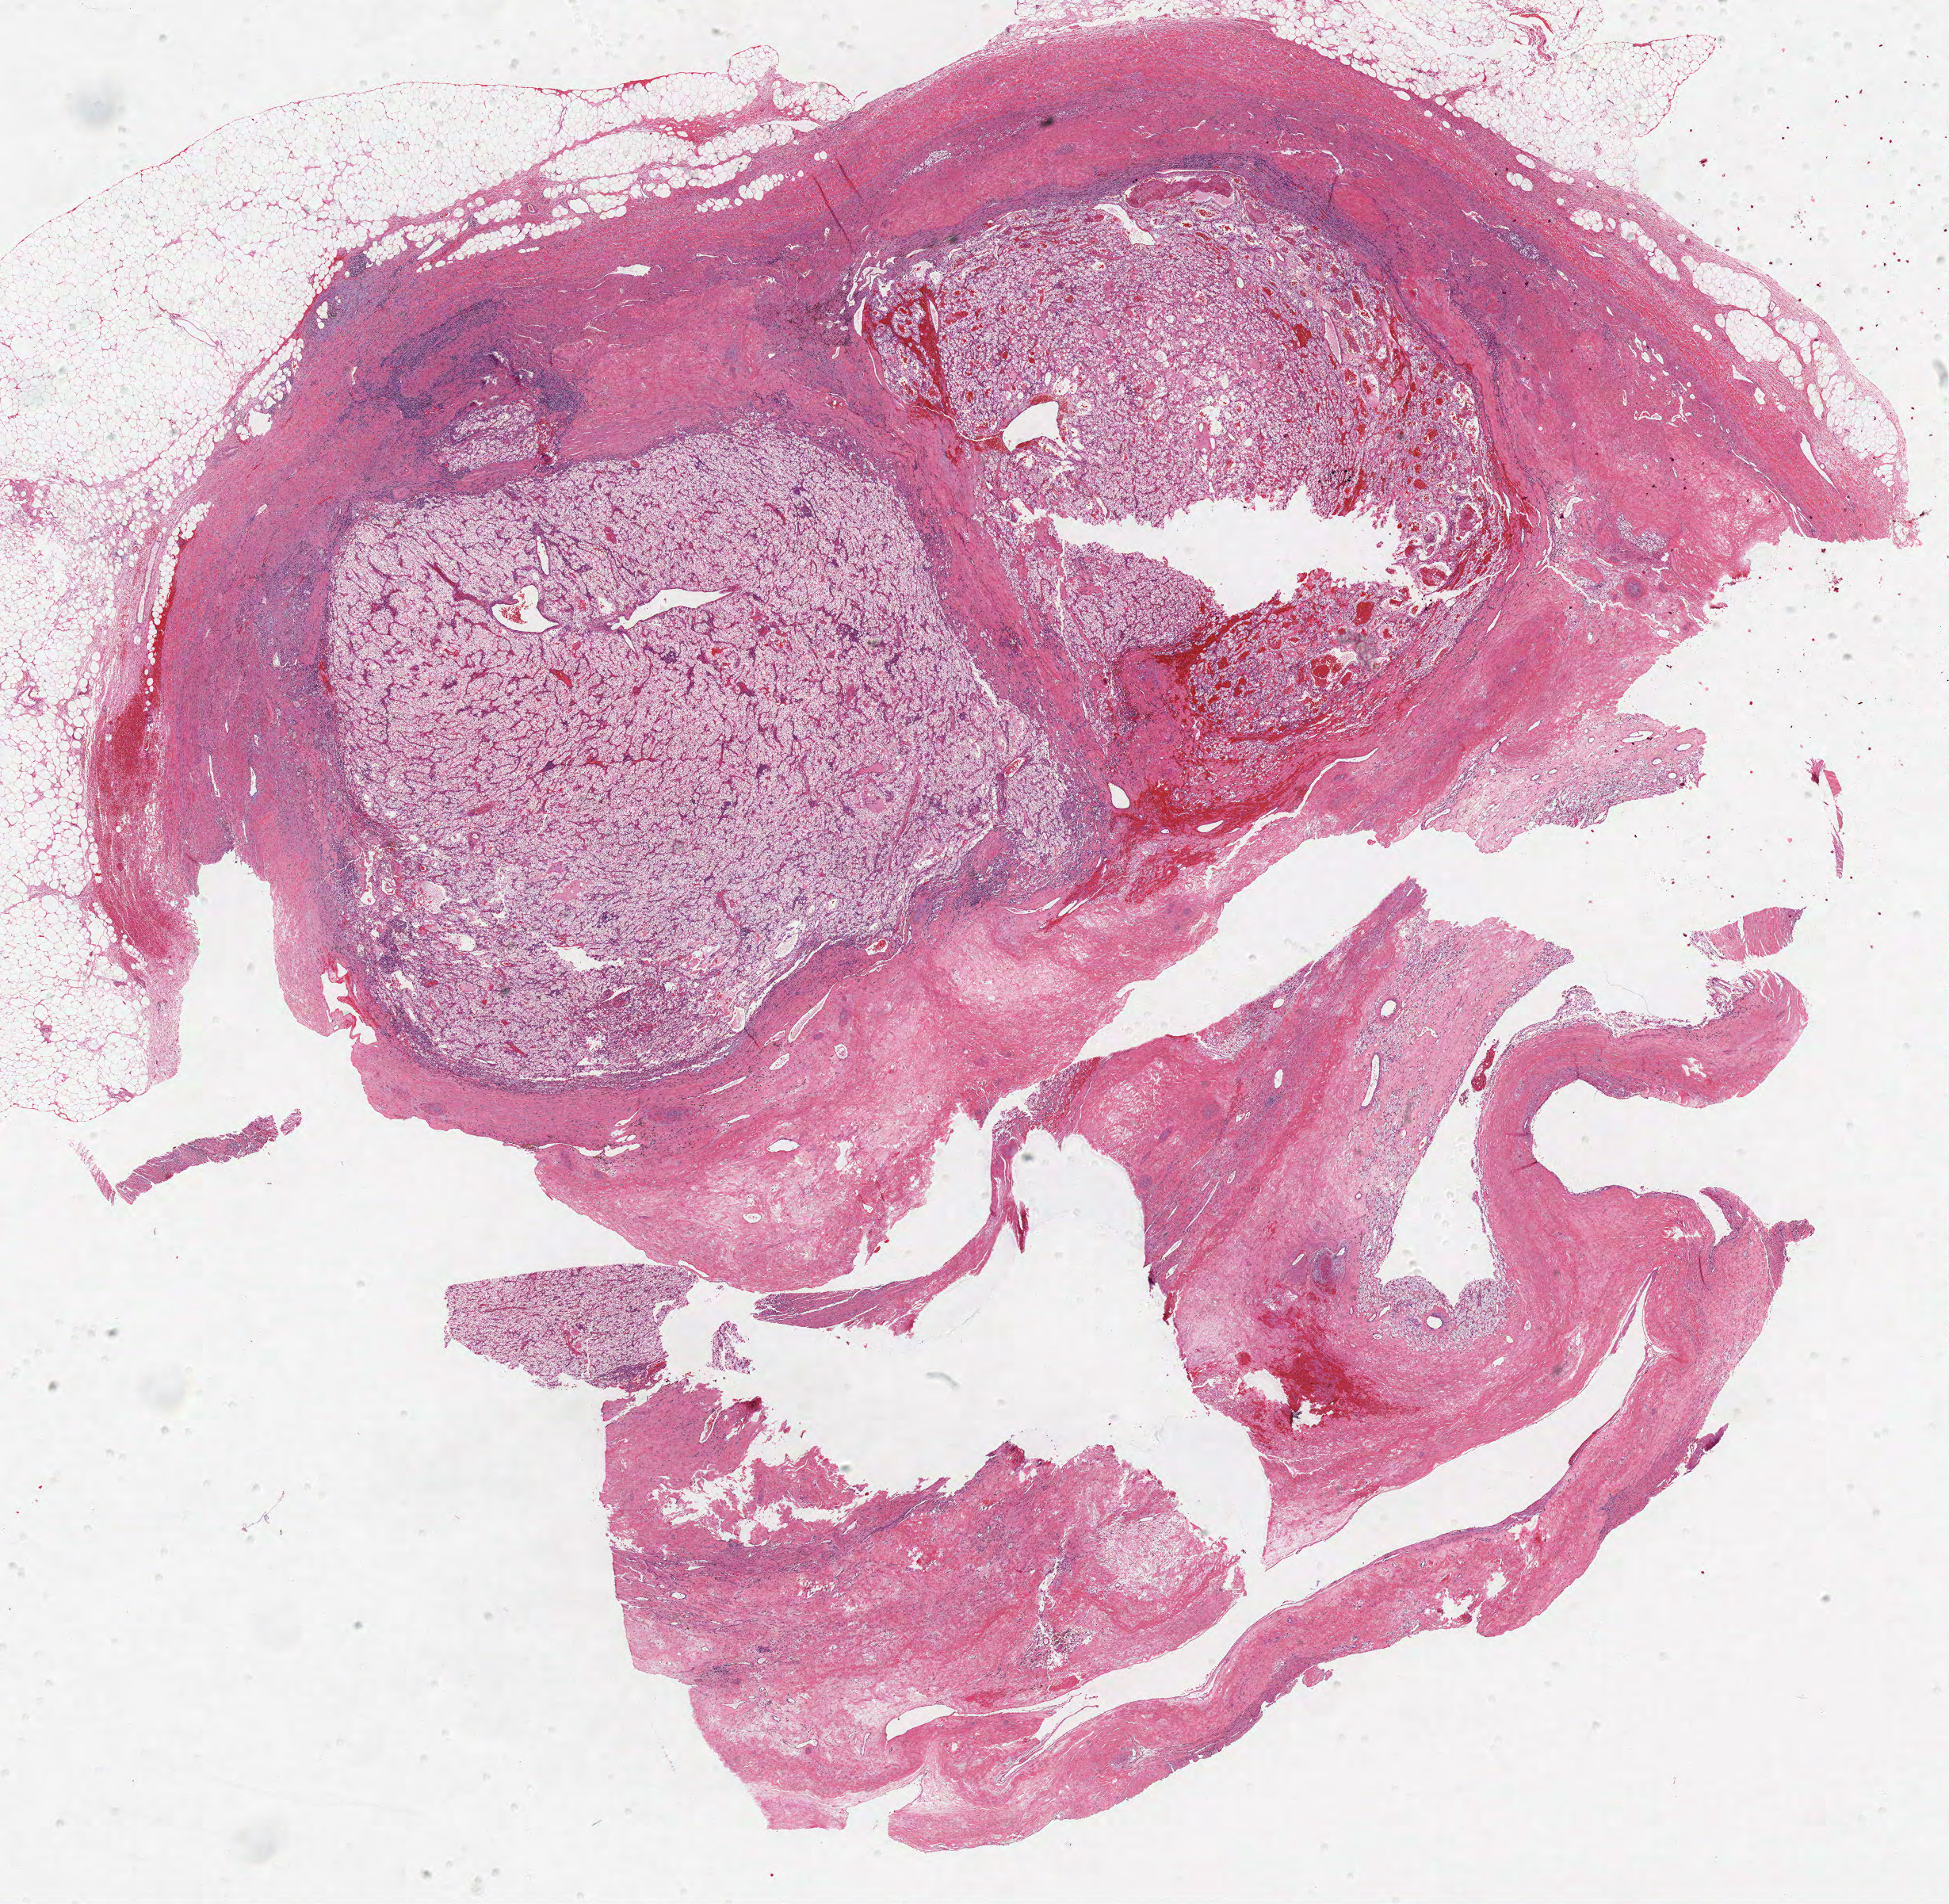
H&E whole-slide image, a low-resolution overview of the entire scanned area, about 19.7 x 19.2 mm (acquisition: 40x scan); formalin-fixed paraffin-embedded (FFPE) diagnostic section; sample: primary tumour, kidney. Male, age 79 years at initial diagnosis. Histologic grade: G2 (moderately differentiated).
- AJCC pathologic stage: III
- diagnosis: Clear cell adenocarcinoma, NOS
- lymph nodes positive (case pathology): 0 of 1 examined
- TNM: T3a N0 M0